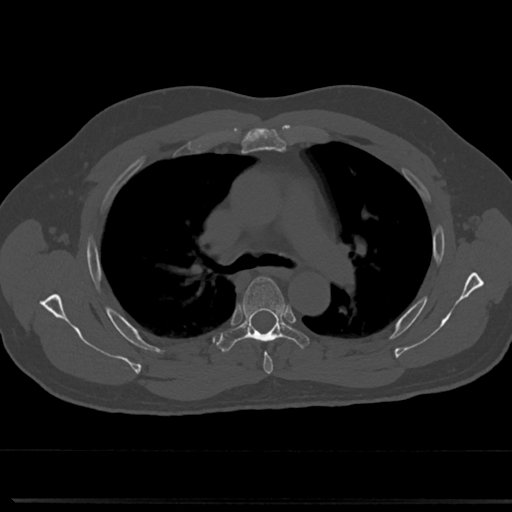
CT including the spine, one axial slice. Slice 510 of 817 in the series (ordered by position). 120 kVp. Bone window (W 1800 / L 400 HU). 0.5 mm slice thickness. 512 × 512 image matrix, field of view 355 × 355 mm. Male patient, age 61 years. Case-level facts recorded for this patient, not image findings: primary cancer: prostate.
Structures marked on this image (semi-automatically segmented with operator editing):
- T4 vertebra: box from (x=241, y=335) to (x=284, y=373) px
- T5 vertebra: (x=218, y=275)–(x=310, y=352)